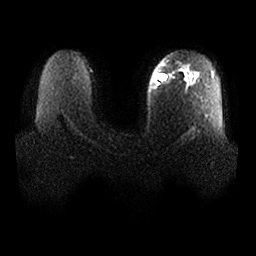
Breast MRI, one axial slice. Slice 20 of 25 in the series (ordered by position). Diffusion-weighted series; image 2 of 4 stored at this slice position (different b-values; order by instance number). 1.5 T. 256 × 256 image matrix, field of view 380 × 380 mm. Female patient.
Structures marked on this image (expert manual segmentation):
- tumour on diffusion-weighted imaging: box from (x=159, y=74) to (x=169, y=81) px